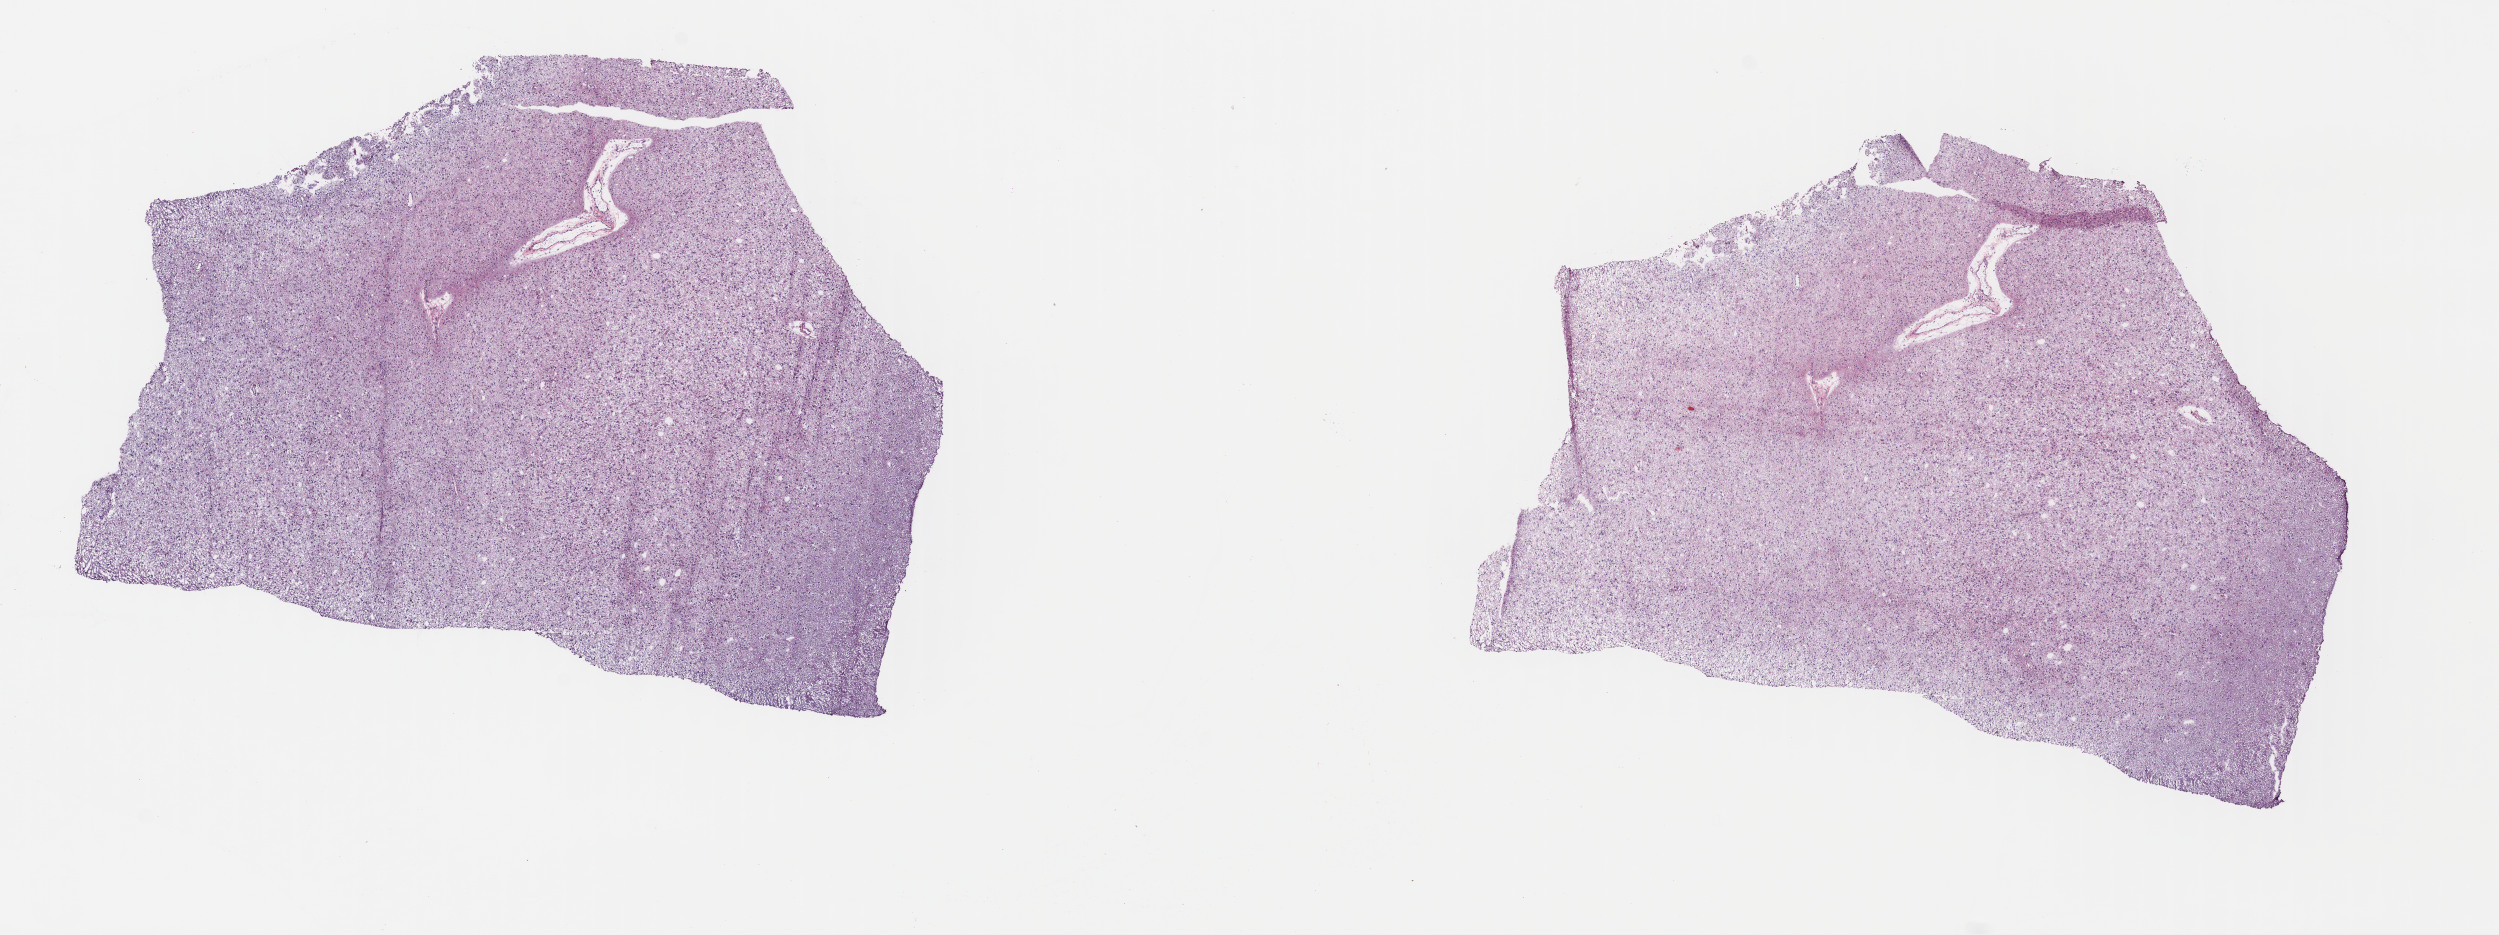
Whole-slide histology image, Hematoxylin and eosin (H&E) stained, low-resolution overview of the scanned area, about 19.6 x 7.3 mm (acquisition: 40x scan), frozen section from the top of the tissue portion, sample: primary tumour, brain. Male, age 20 years at initial diagnosis. Histologic grade: G2 (moderately differentiated). Pathologist review of this section (percent, as recorded): tumour cells 70%, tumour nuclei 75%, normal cells 10%, stromal cells 20%, necrosis 0%. Infiltration values recorded for this section: lymphocyte infiltration 0%, monocyte infiltration 0%, neutrophil infiltration 0%.
* diagnosis: Mixed glioma (cerebrum)